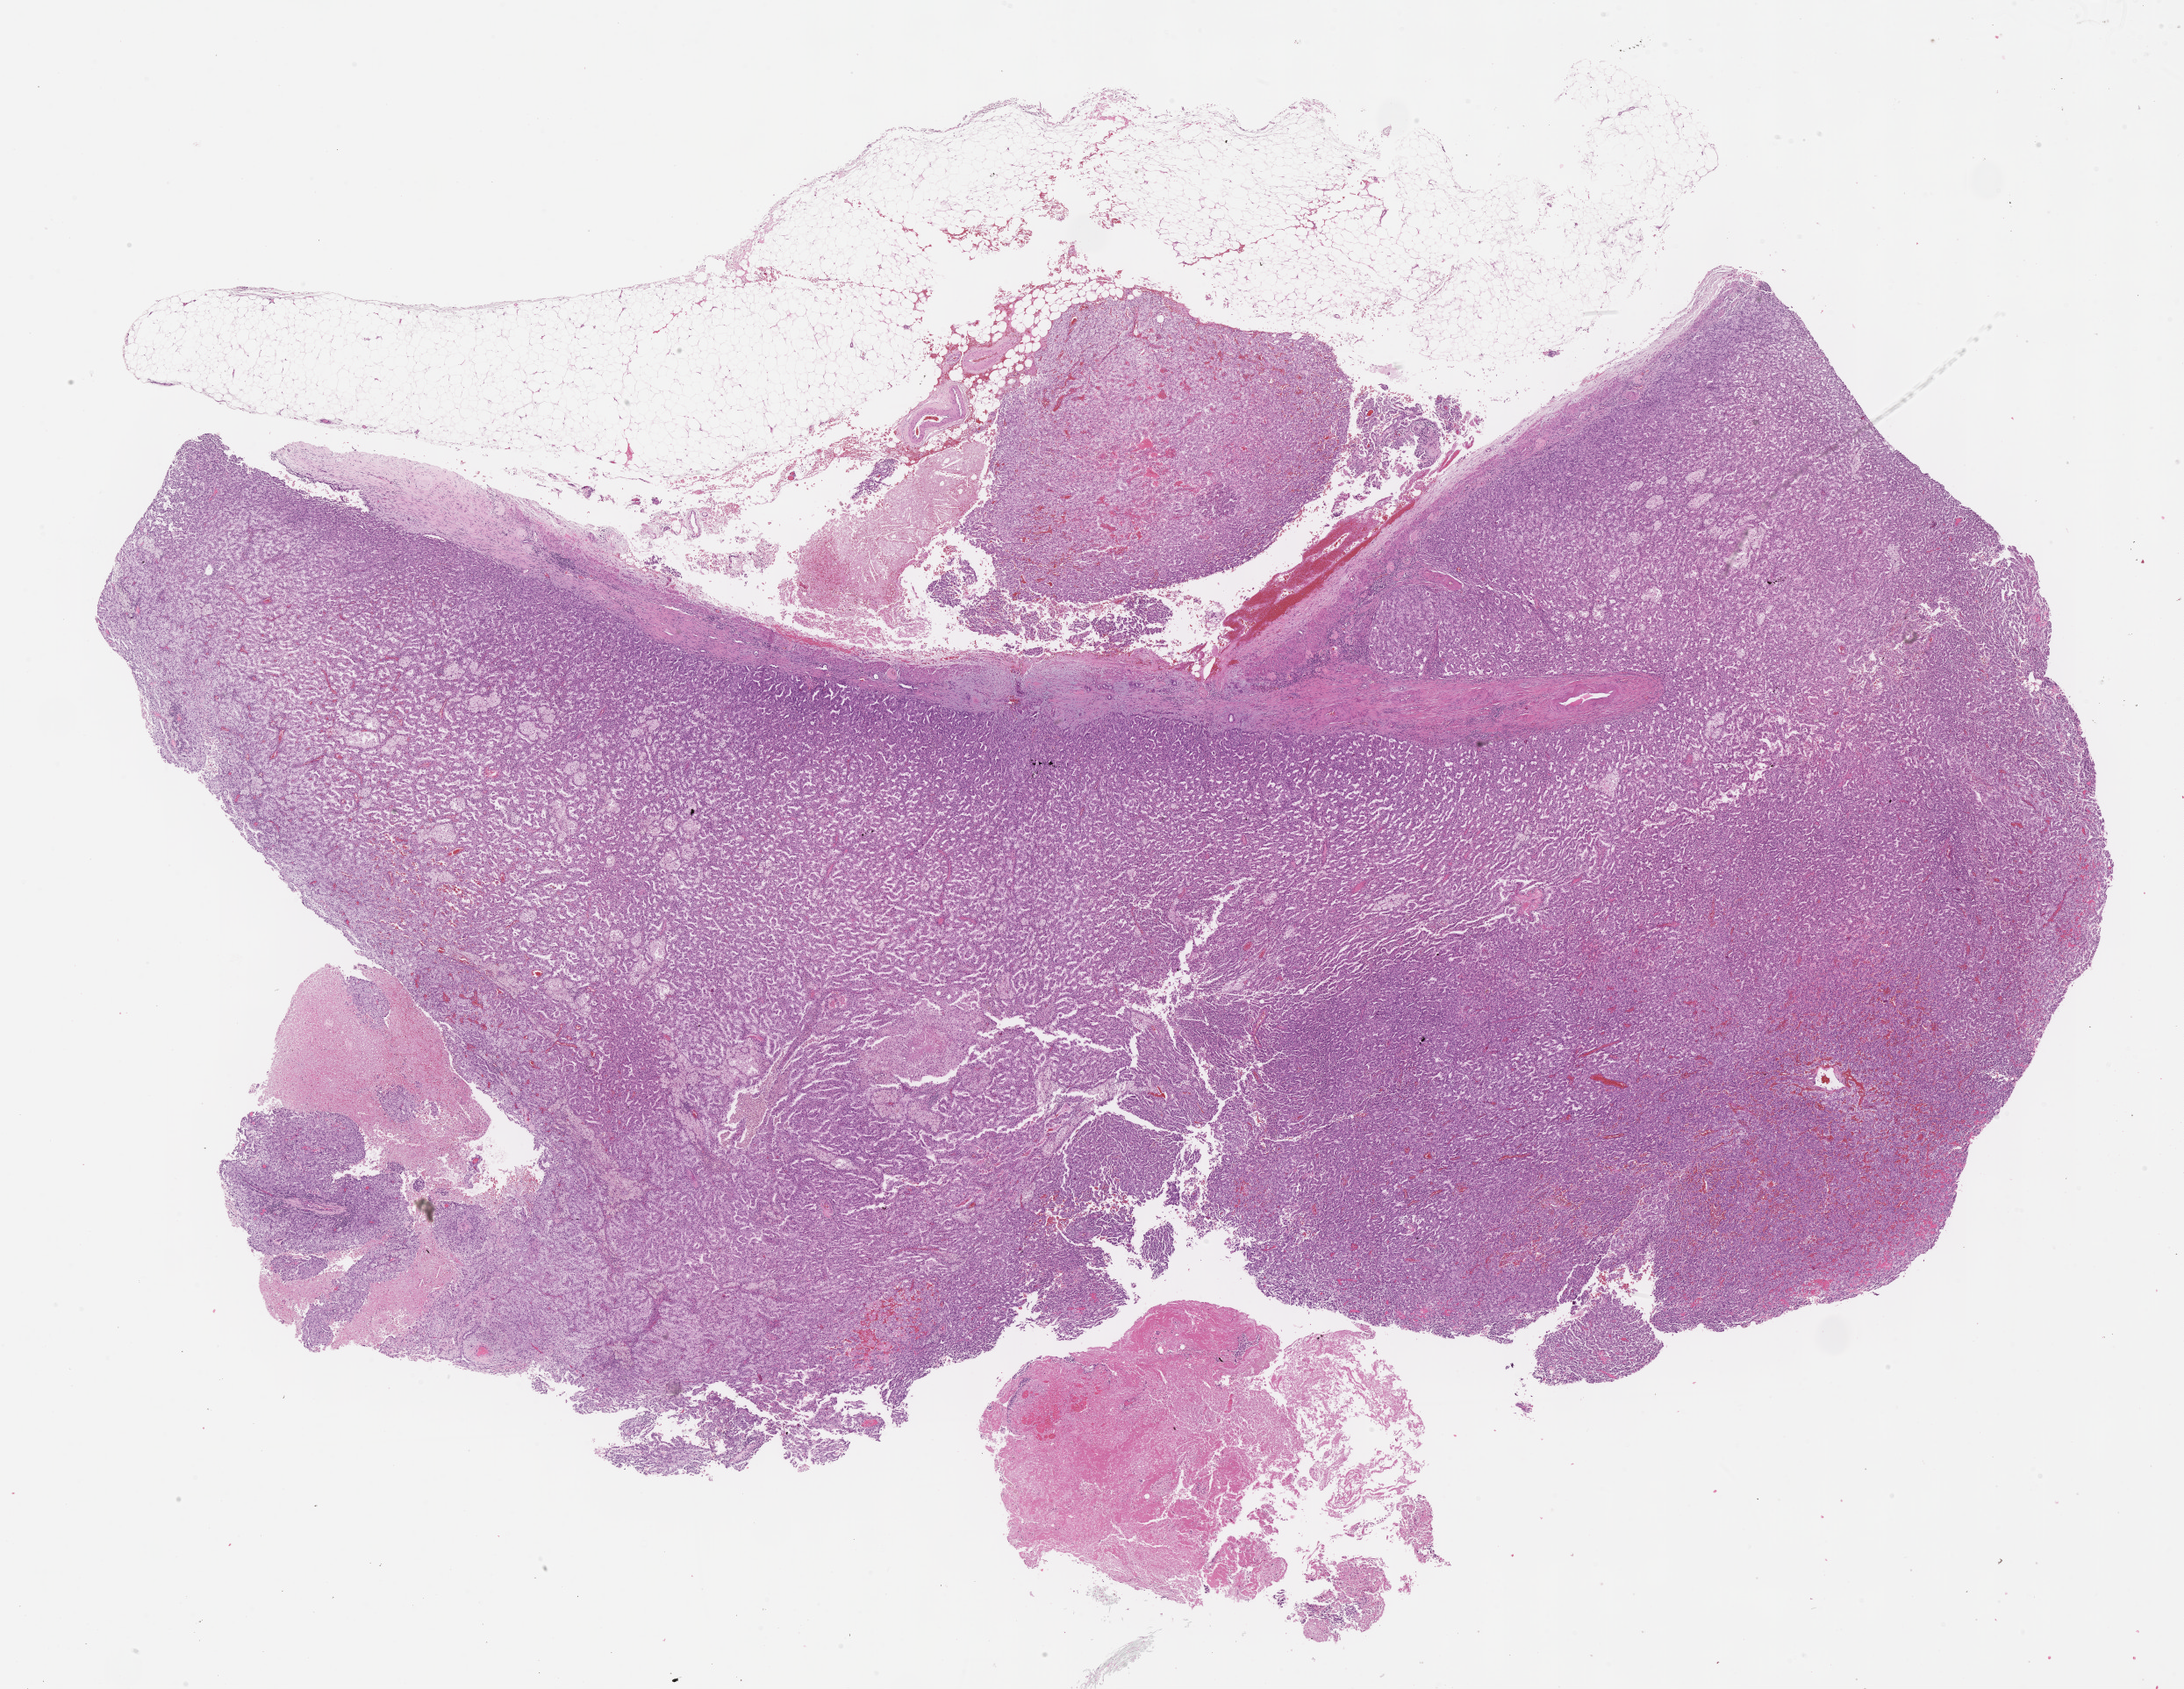
Whole-slide histology image, Hematoxylin and eosin (H&E) stained, low-resolution overview of the scanned area, about 20.1 x 15.6 mm; formalin-fixed paraffin-embedded (FFPE) diagnostic section; kidney, primary tumour sample. Patient: female, age at initial diagnosis 74 years.
AJCC pathologic stage: I (7th edition). Laterality: left. Histologic diagnosis: Papillary adenocarcinoma, NOS.